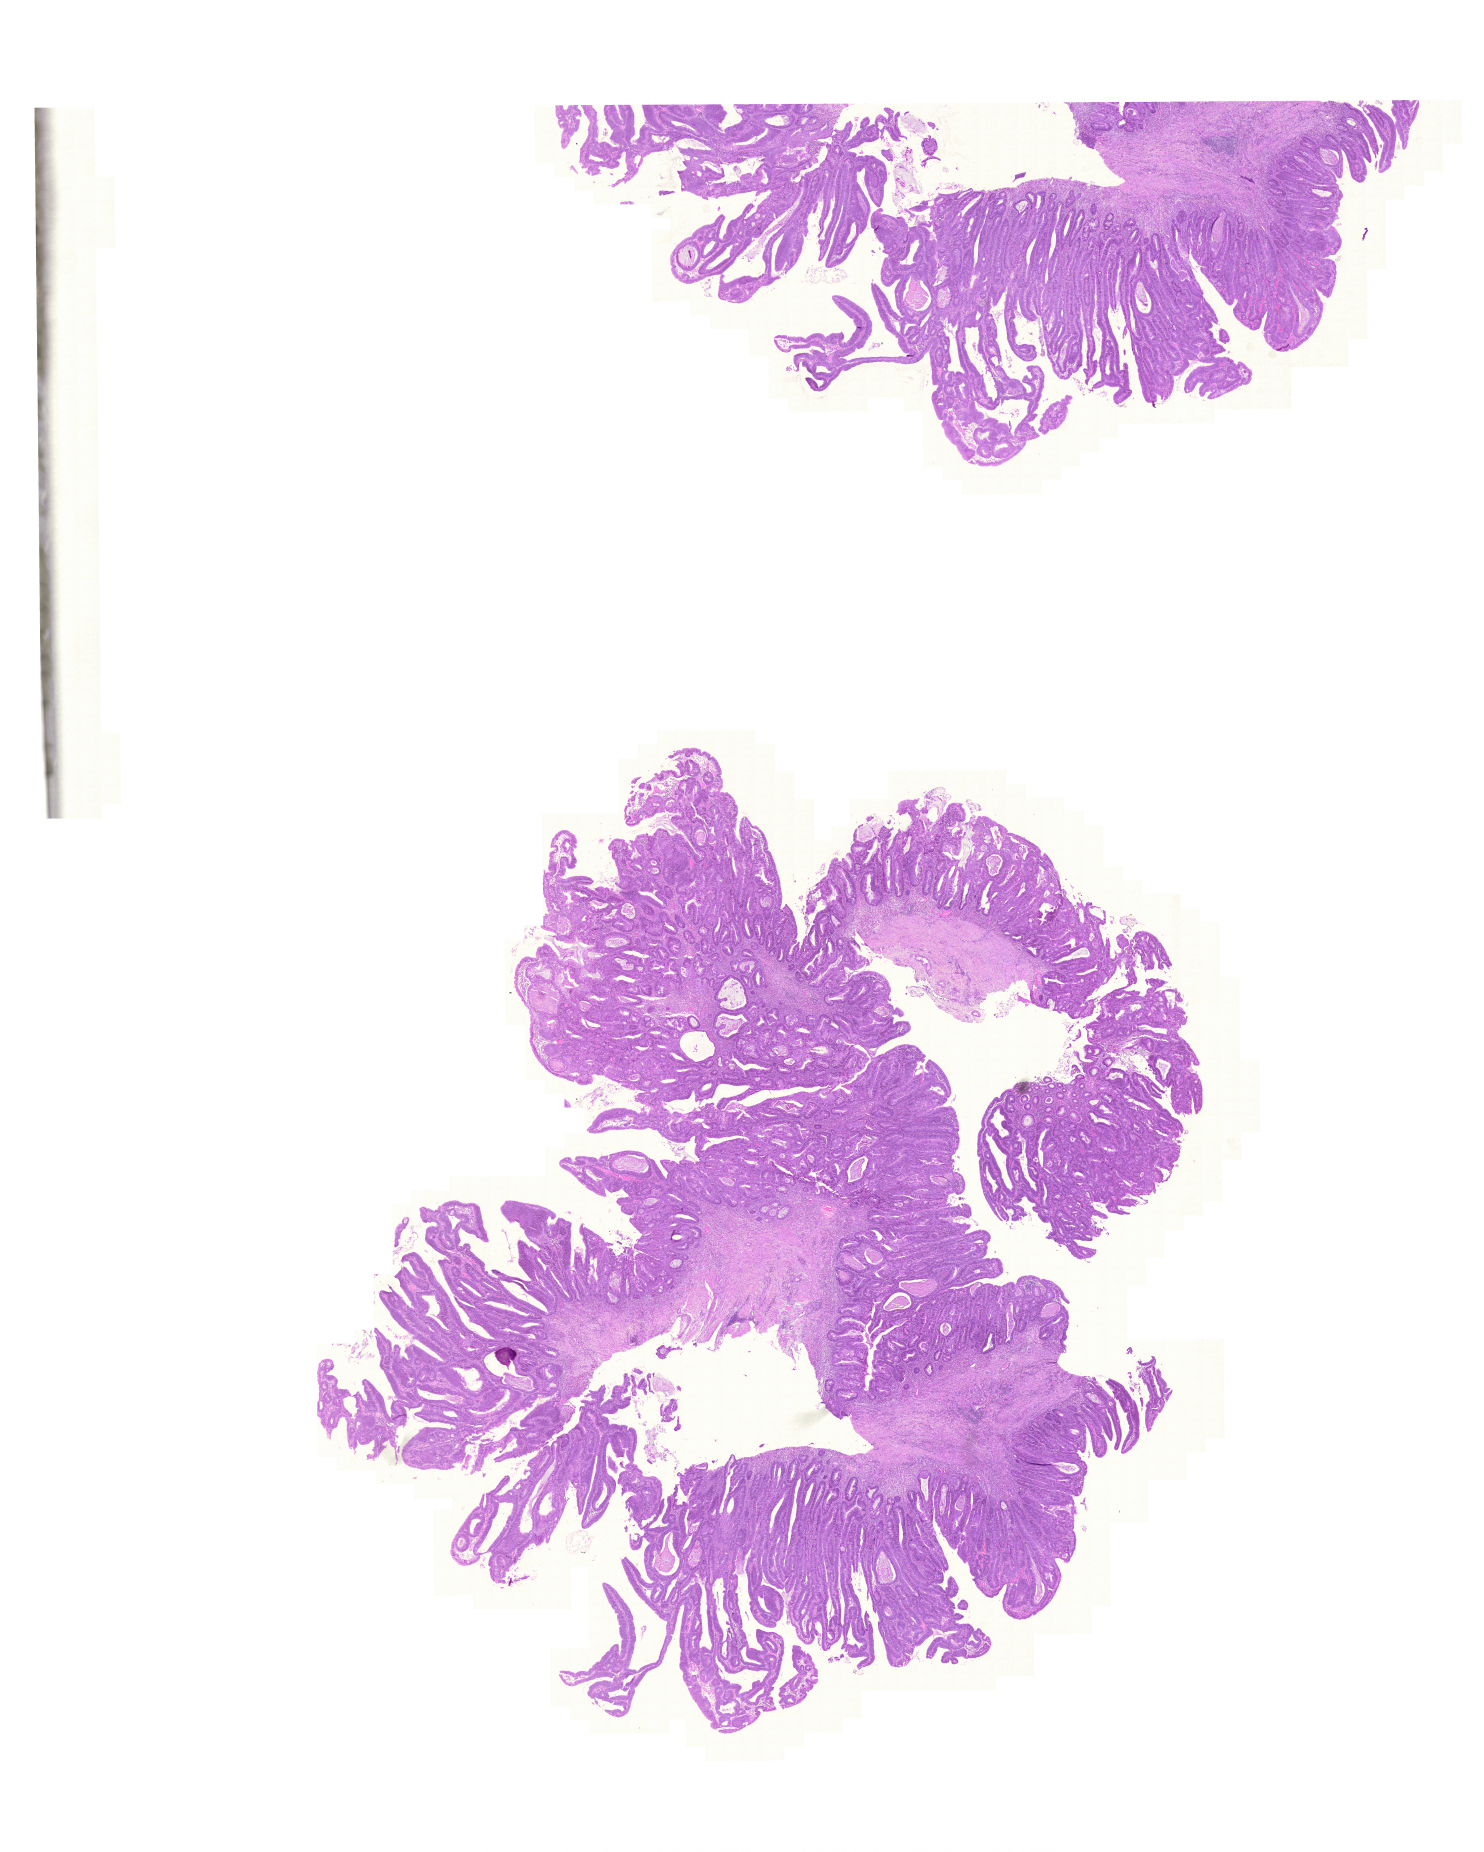
H&E whole-slide image — low-resolution overview of the scanned area, about 22.1 x 27.6 mm (slide scanned at 20x), formalin-fixed paraffin-embedded (FFPE) diagnostic section, primary tumour sample from the colon. Male patient; age at initial diagnosis 59 years.
* AJCC pathologic stage: I (5th edition)
* lymph nodes positive (case pathology): 0 of 15 examined
* TNM: T2 N0 M0
* pathologic diagnosis: Adenocarcinoma, NOS (cecum)